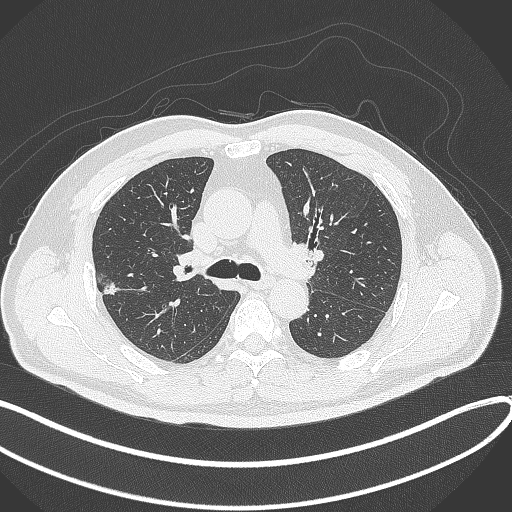
Chest CT, one axial slice; slice 221 of 372 in the series (ordered by position); reconstruction kernel B70f; lung window (W 1500 / L -600 HU); 1 mm slice thickness; 512 × 512 image matrix, field of view 400 × 400 mm. Patient: male, 60 years. From the clinical record (not read from this slice): clinical TNM (as recorded): T1c N0 M0.
Structures marked on this image (bounding box drawn by a radiologist):
- lung tumour (recorded histology: adenocarcinoma): box from (x=98, y=273) to (x=125, y=299) px